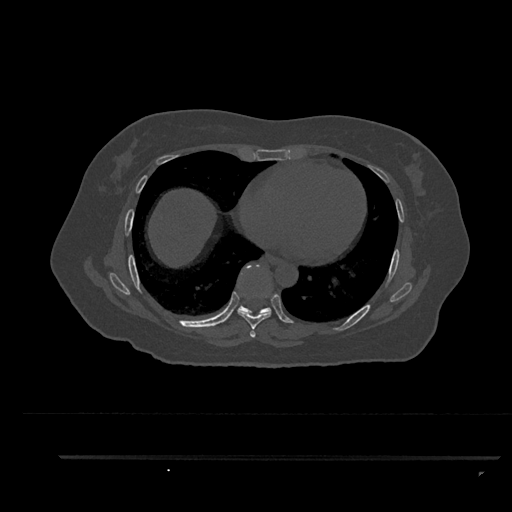
CT including the spine, one axial slice. Position 491 of 797 along the scan axis. Reconstruction kernel Br40s/3. 120 kVp. Bone window (W 1800 / L 400 HU). 512 × 512 image matrix, field of view 408 × 408 mm. Female patient, age 44 years. From the clinical record (not read from this slice): primary cancer: renal.
Structures marked on this image (semi-automatically segmented with operator editing):
- T6 vertebra: box from (x=251, y=335) to (x=255, y=337) px
- T7 vertebra: (x=237, y=264)–(x=271, y=338)
- T8 vertebra: (x=237, y=265)–(x=271, y=316)